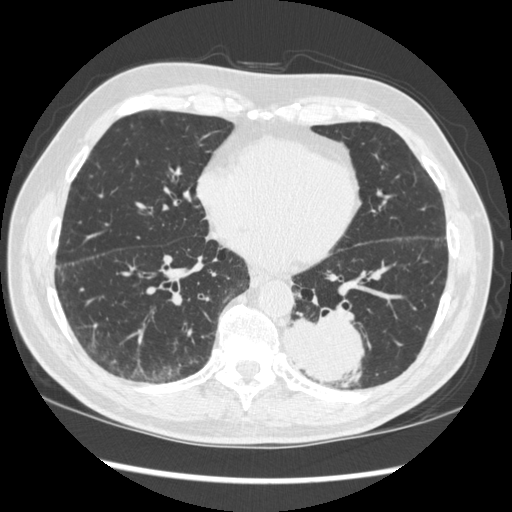
Low-dose screening chest CT, one axial slice. Position 125 of 348 along the scan axis. Reconstruction kernel STANDARD. 120 kVp. Lung window (W 1500 / L -600 HU). 1.25 mm slice thickness. 512 × 512 image matrix, field of view 360 × 360 mm.
Outlined on this slice (expert manual segmentation):
- lesion 1 (tumor, lower lobe of left lung): bounding box [x1, y1, x2, y2] px = [285, 312, 365, 388]